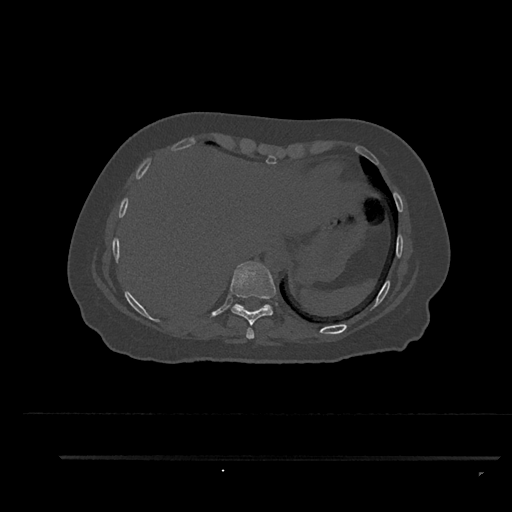
CT including the spine, one axial slice; reconstruction kernel Br40s/3; bone window (W 1800 / L 400 HU); 512 × 512 image matrix, field of view 408 × 408 mm. Patient: female, 44 years. Case-level facts recorded for this patient, not image findings: primary cancer: renal.
Structures marked on this image (semi-automatic segmentation, software-assisted and operator-edited):
- T10 vertebra: bounding box [x1, y1, x2, y2] px = [235, 304, 272, 308]
- T8 vertebra: [246, 327, 255, 339]
- T9 vertebra: [230, 261, 276, 326]